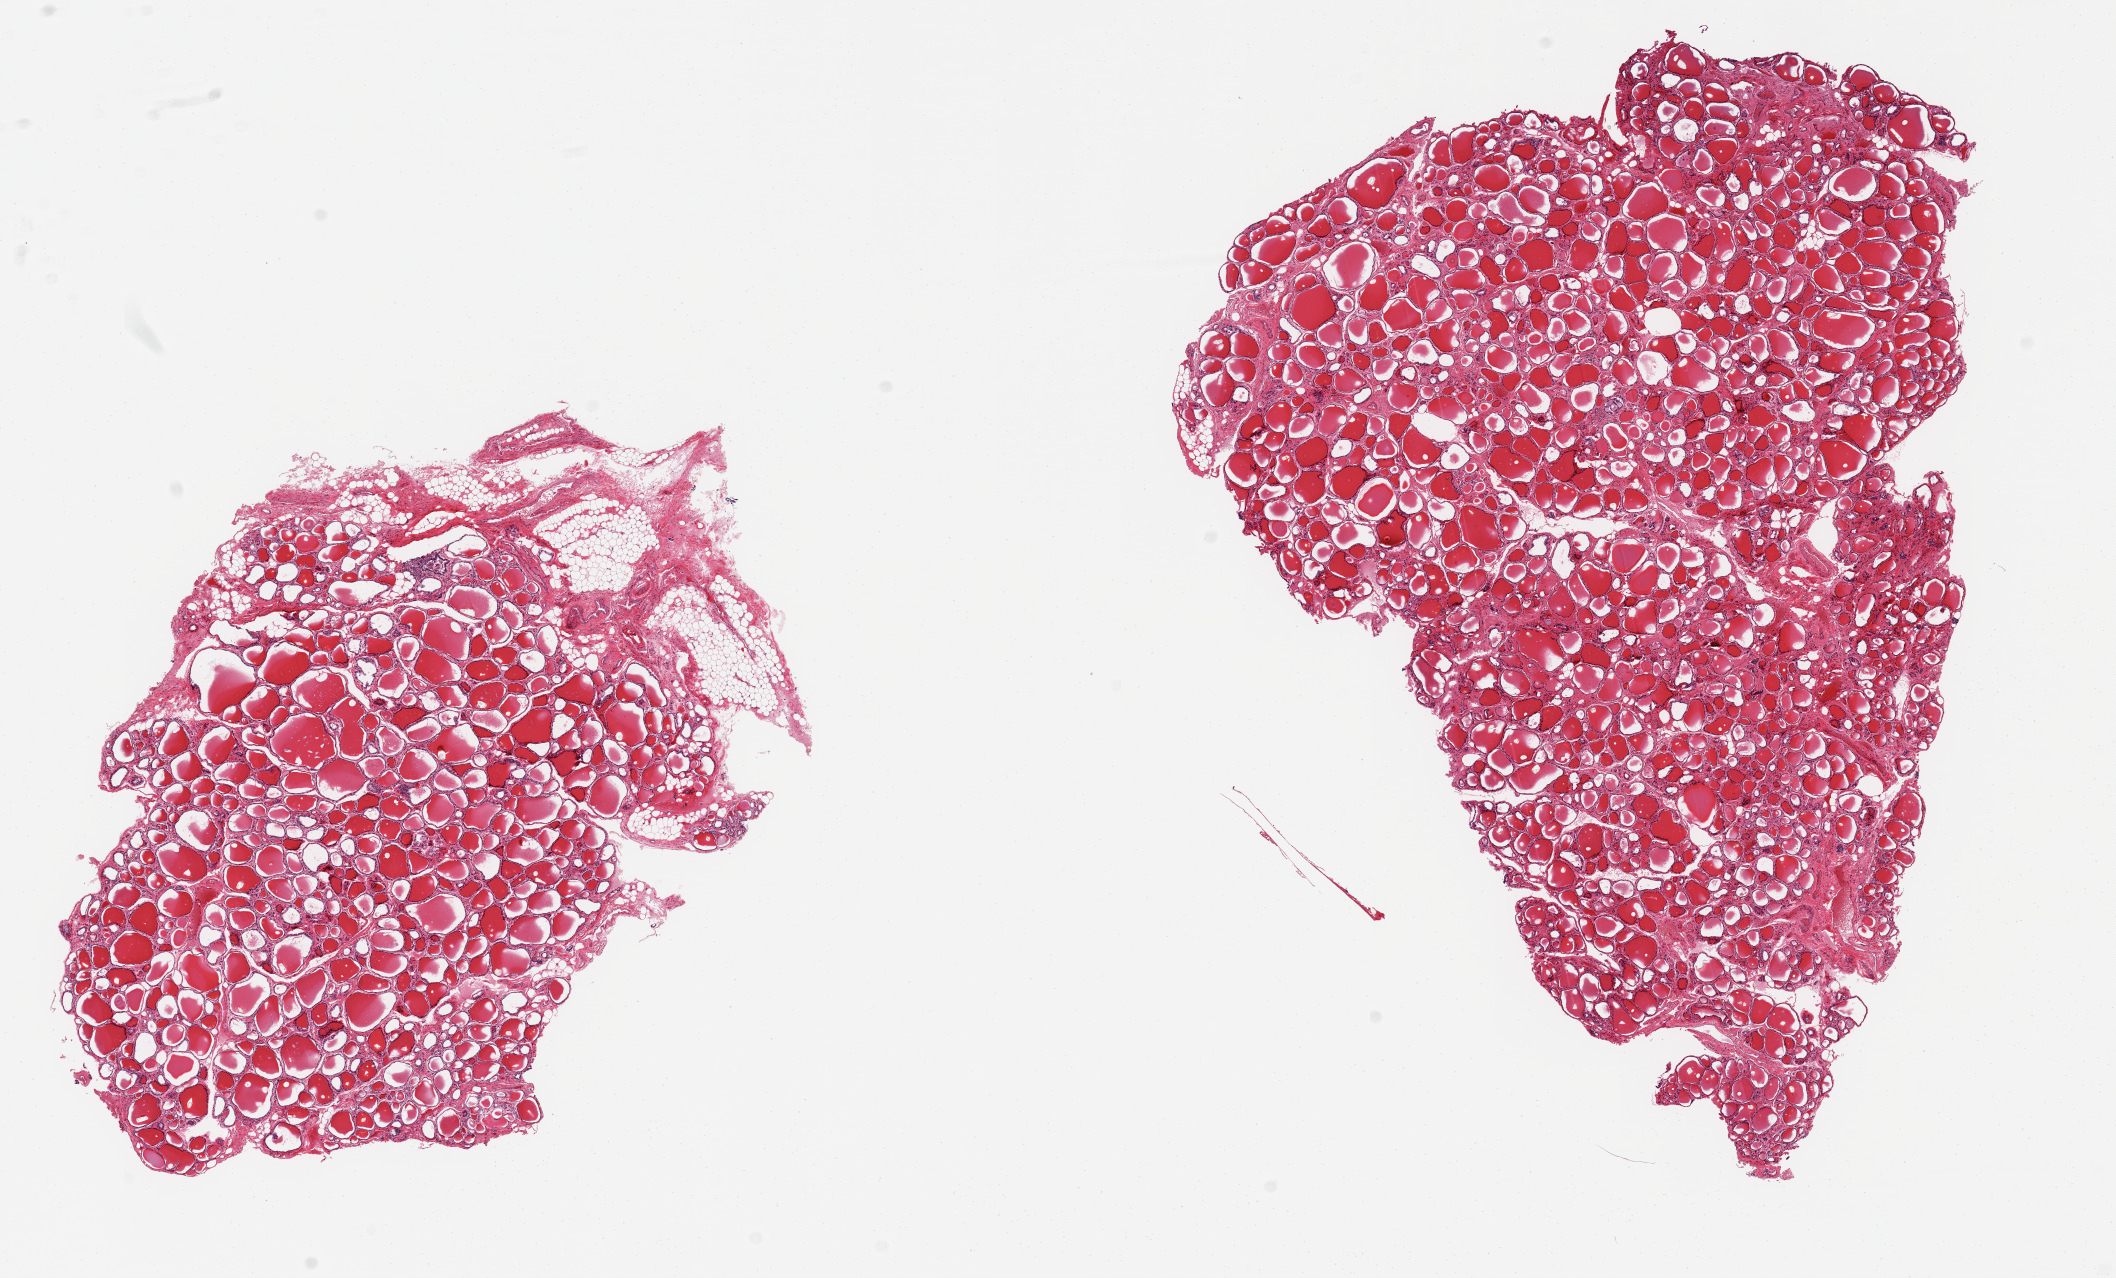
Whole-slide image, hematoxylin and eosin (H&E) stain, whole scanned area (about 16.7 x 10.1 mm) shown as a low-resolution overview. PAXgene-fixed, paraffin-embedded tissue. Section of thyroid (target tissue). Donor tissue sample. Donor sex: male.
Reviewer comment on this tissue sample: 2 pieces, no abnormalities, adherent nubbin of fat/fibrous tissue up to ~2mm.